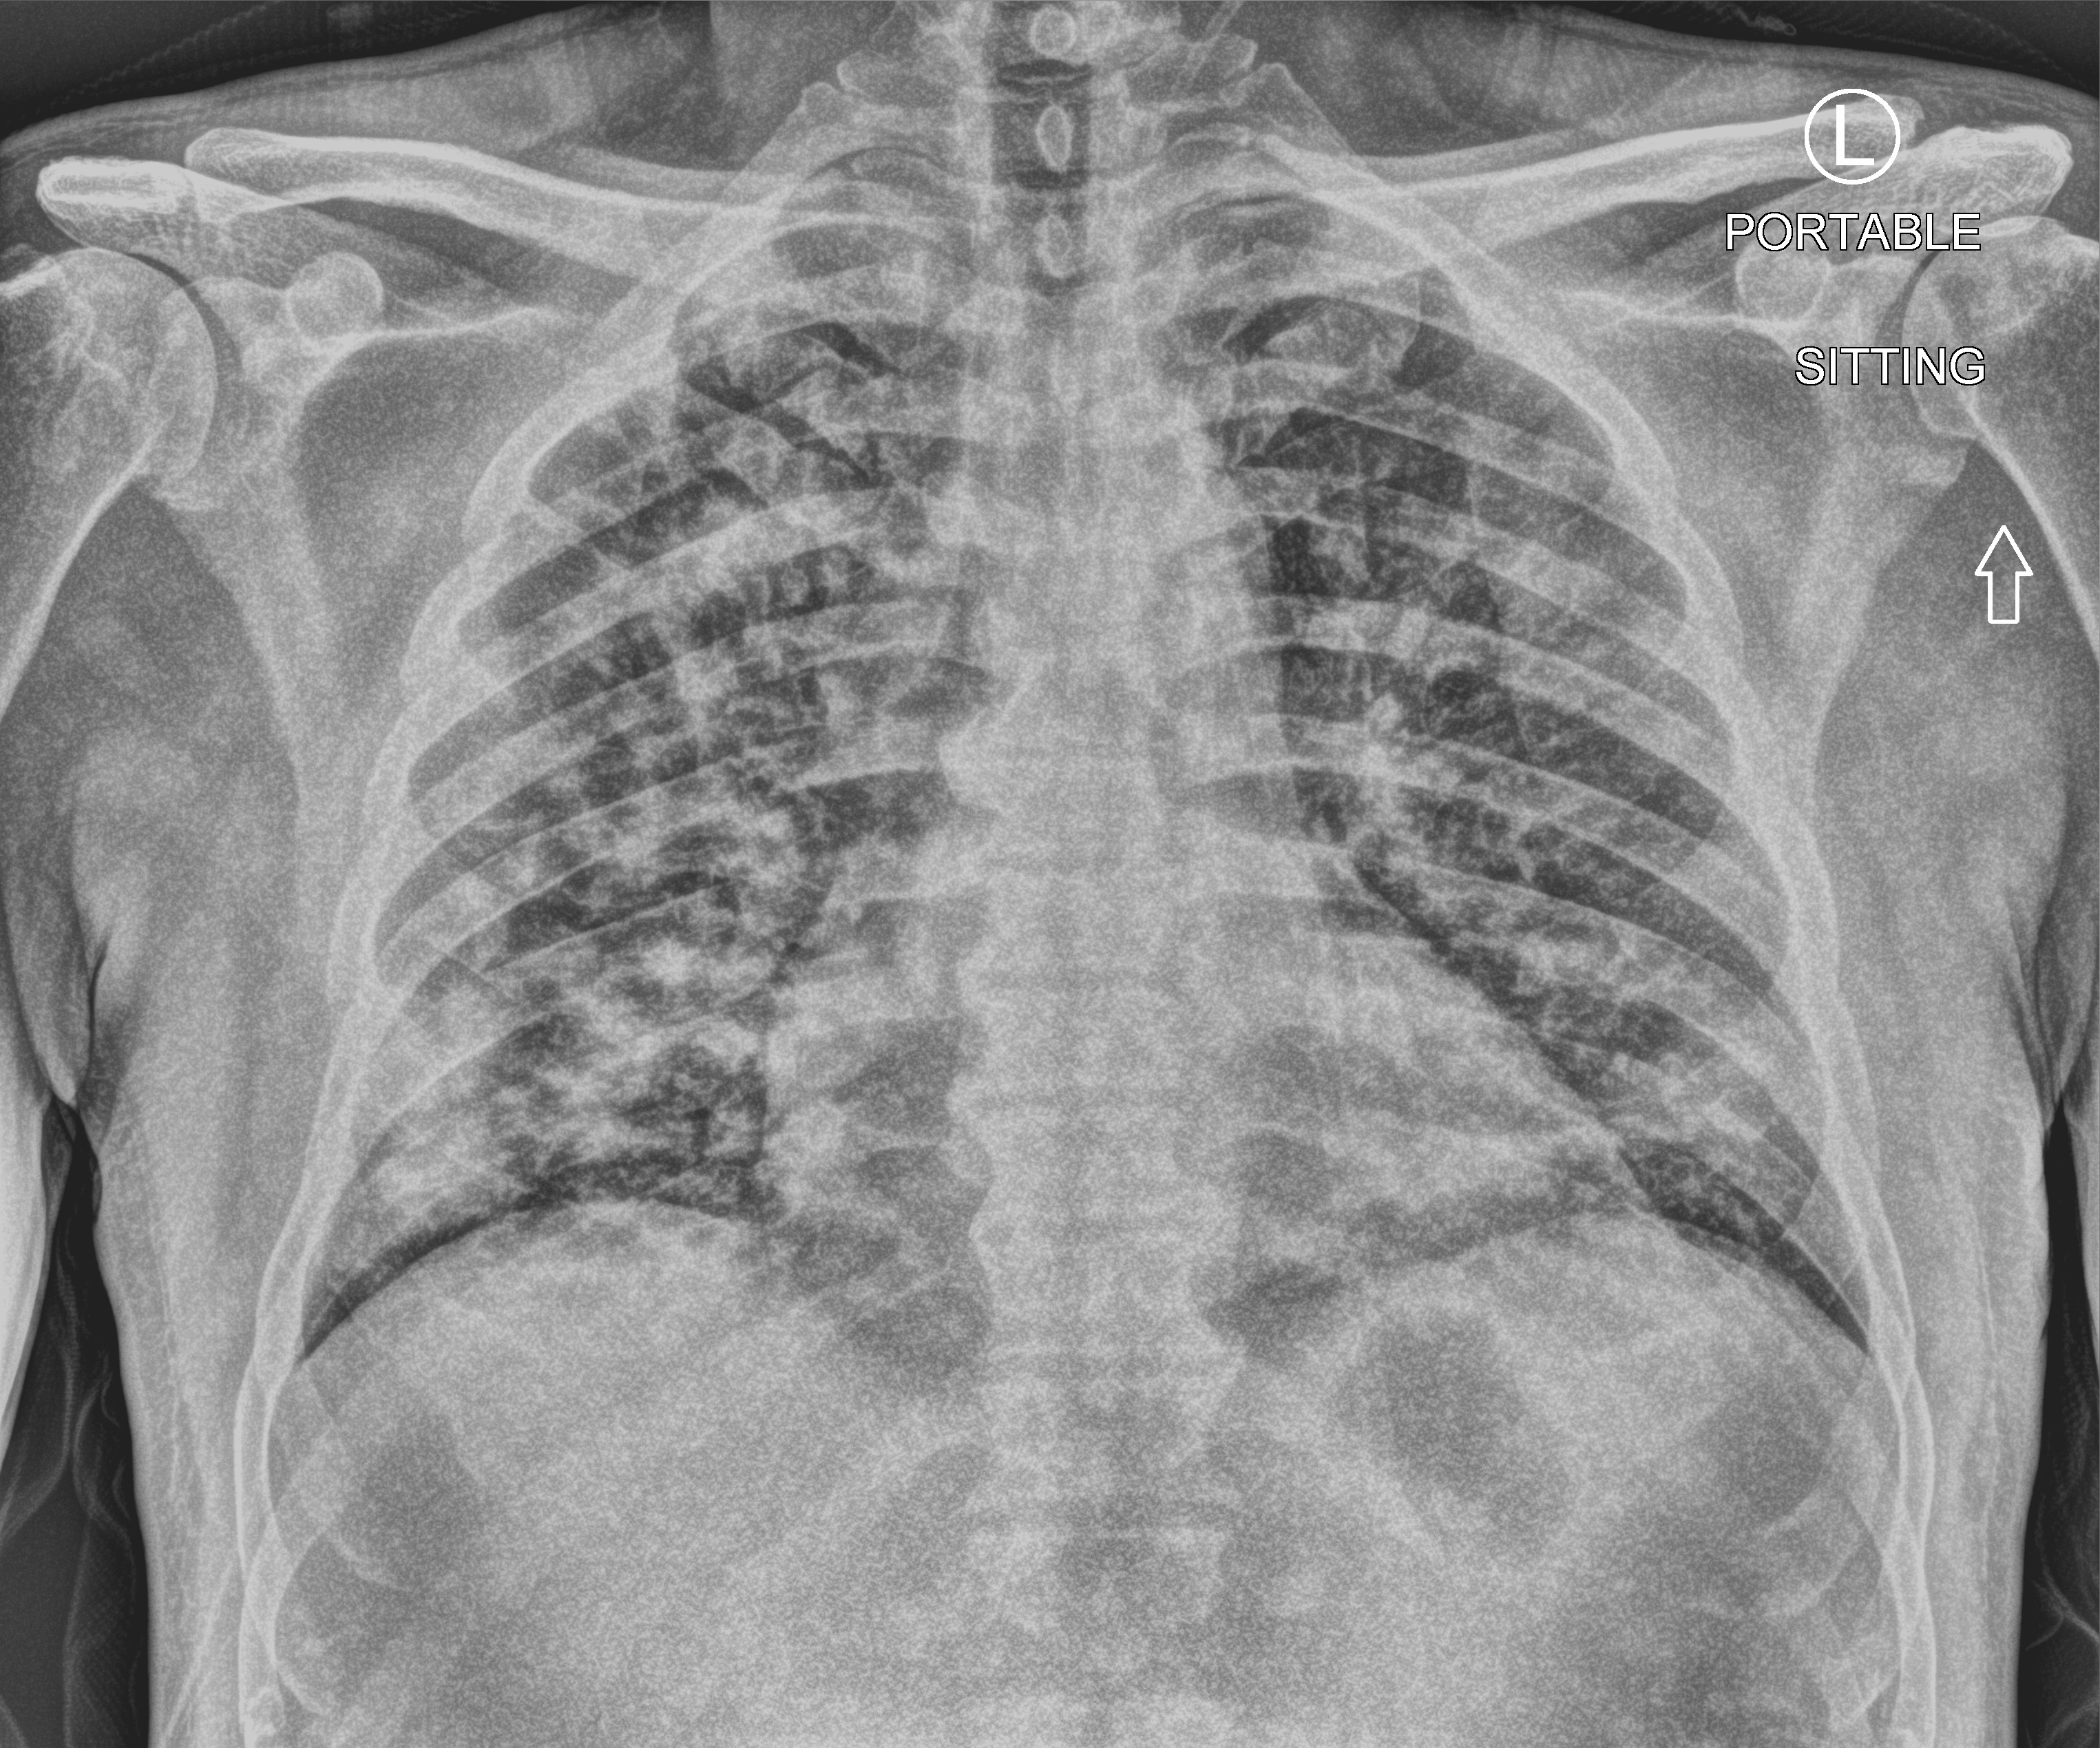
Chest X-ray (portable), anteroposterior (AP) projection. Patient hospitalised with COVID-19; male, aged 18–59 years.
Hospital-stay facts (about this admission, not read from this image; timing relative to this image not recorded): admitted to intensive care during this hospital stay: no; hypertension (admission record): yes.